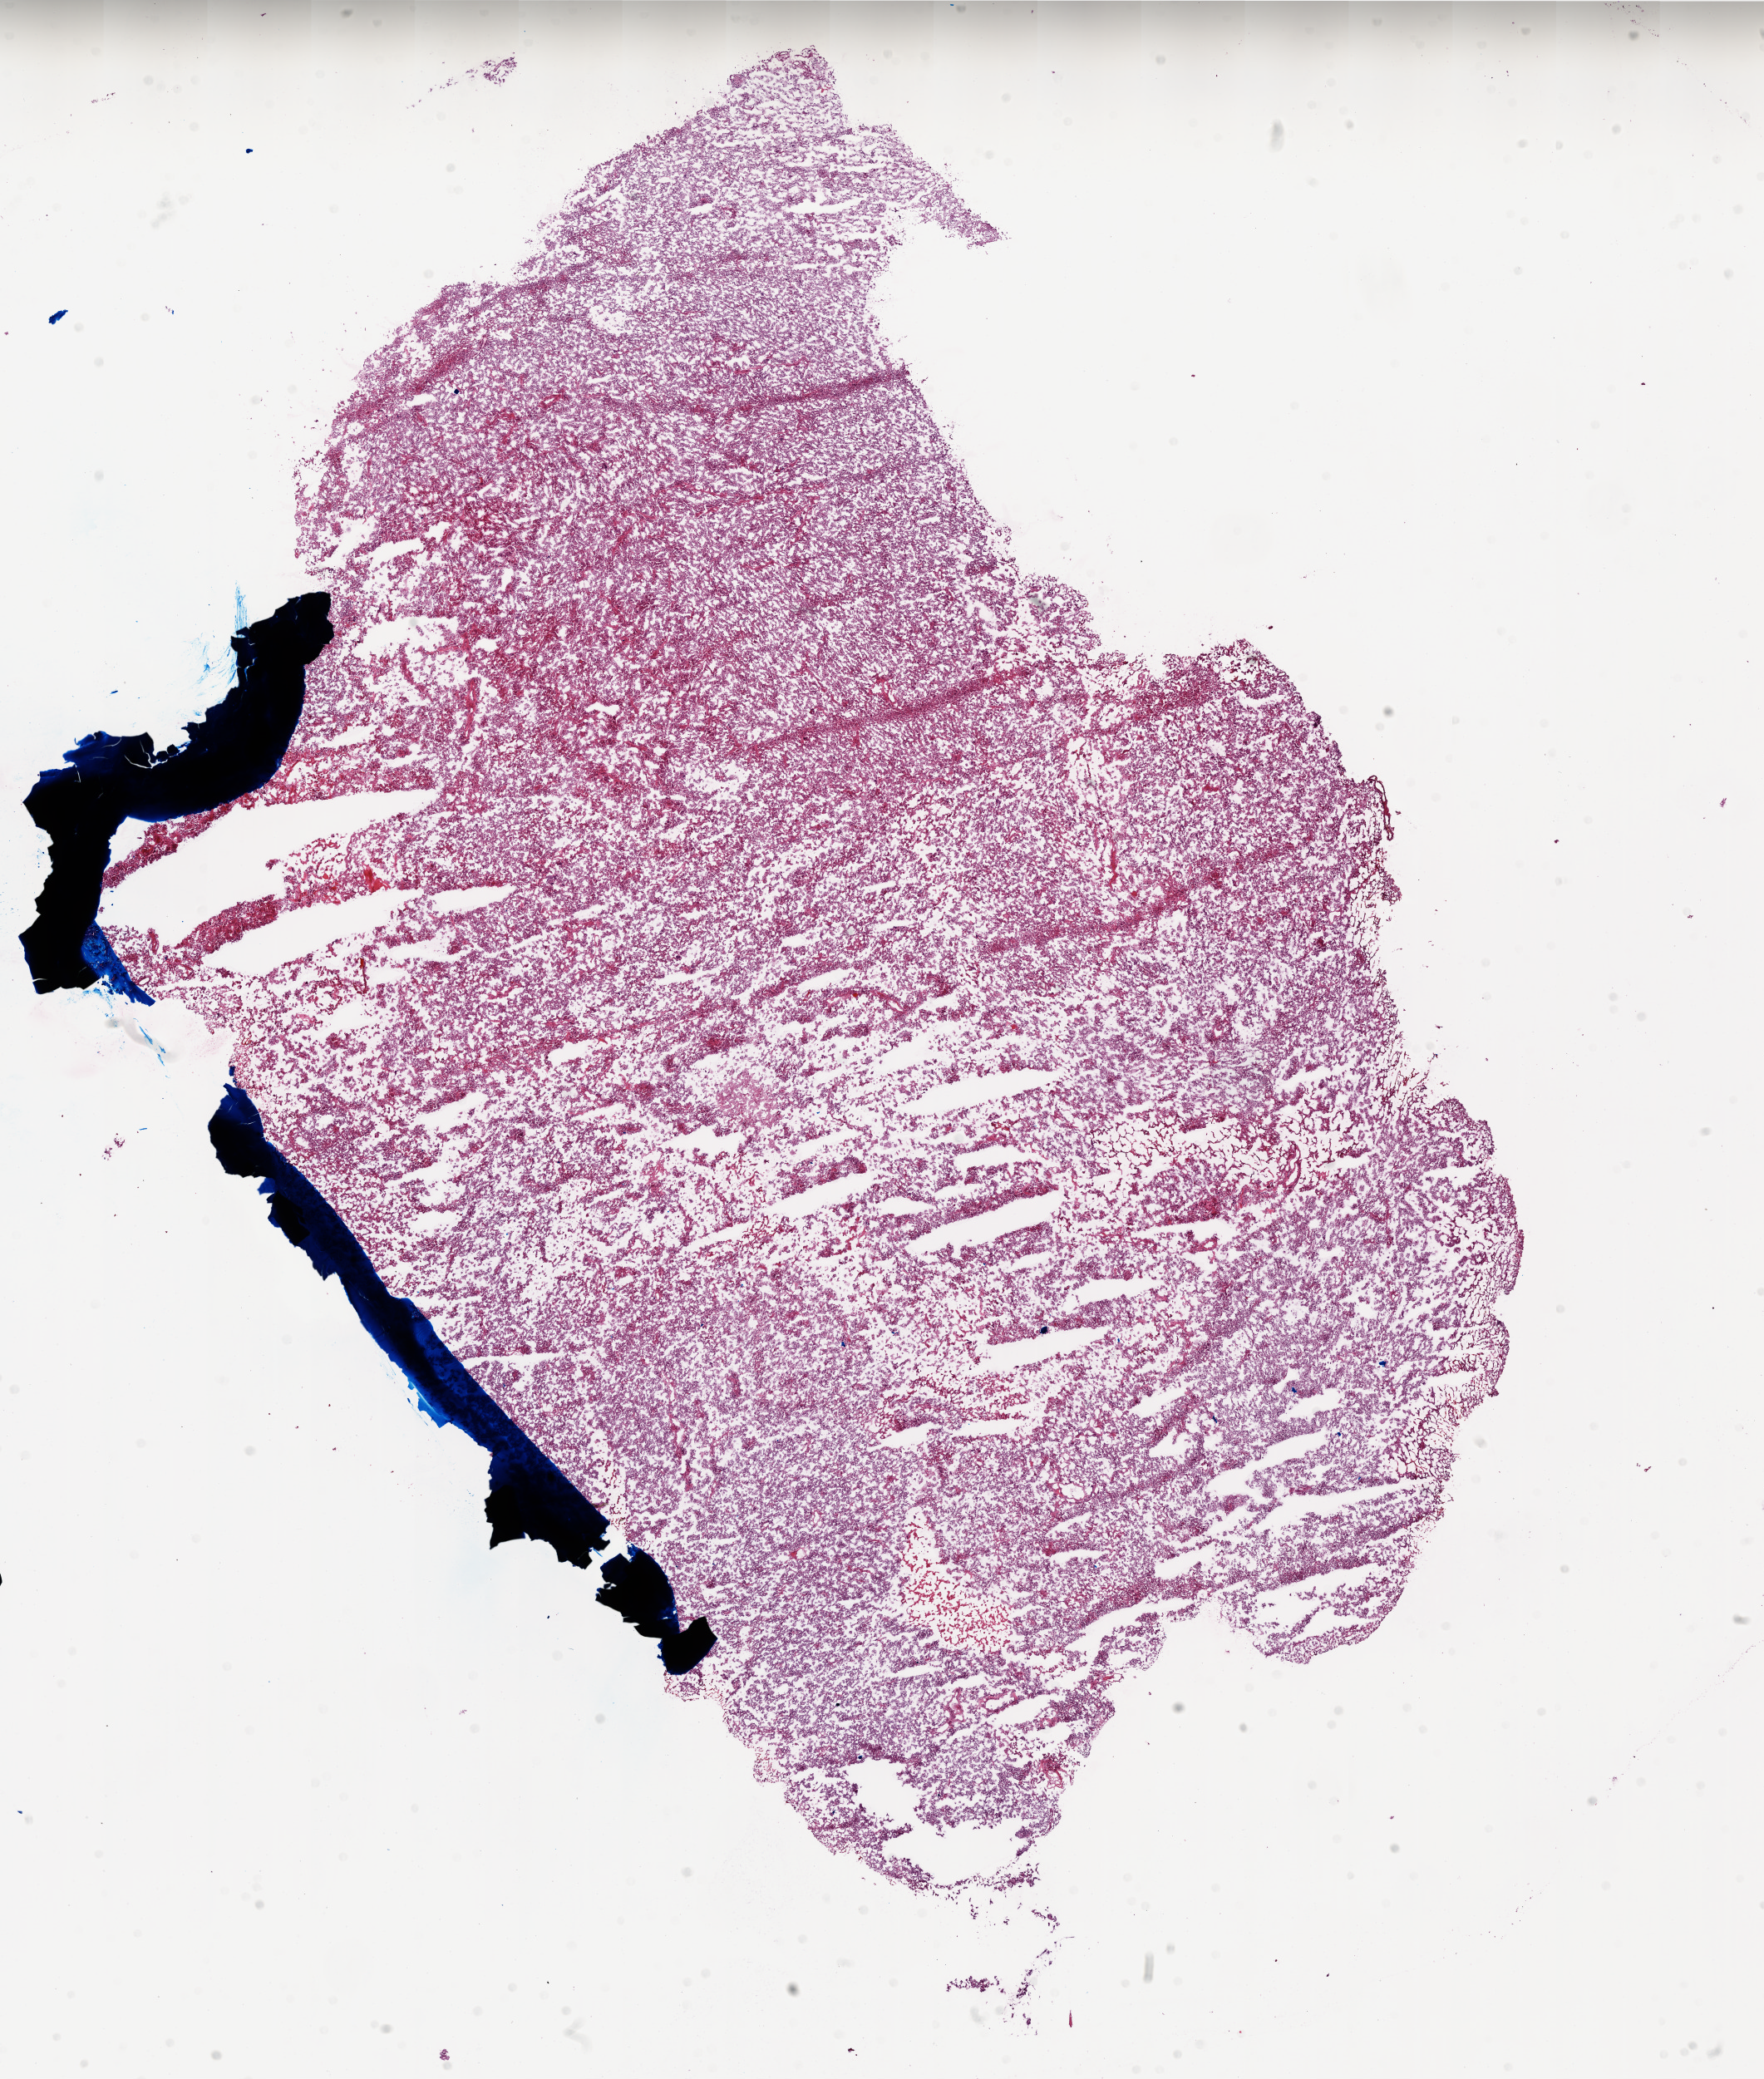
Digitized Hematoxylin and eosin (H&E) stained tissue section (whole slide), whole scanned area (about 17.0 x 20.0 mm, slide scanned at 20x) shown as a low-resolution overview. Frozen section from the top of the tissue portion. Brain, primary tumour sample. Patient: male, age at initial diagnosis 41 years. Composition of this section per pathologist review: tumour cells 90%, tumour nuclei 100%, normal cells 0%, stromal cells 0%, necrosis 10%. Infiltration values recorded for this section: lymphocyte infiltration 0%.
Pathologic diagnosis: Glioblastoma.